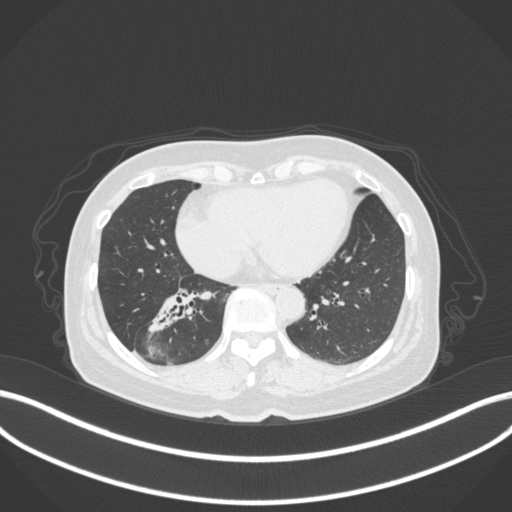
Chest CT, one axial slice; position 143 of 429 along the scan axis; reconstruction kernel B31f; lung window (W 1500 / L -600 HU); 512 × 512 image matrix. Female patient, age 67 years. From the clinical record (not read from this slice): clinical TNM (as recorded): T1c N1 M0; histopathological grade: G2-3.
Annotated regions visible in this slice (rectangle marked by the reading radiologist):
- lung tumour (recorded histology: adenocarcinoma): bounding box <141,282,200,335> (left, top, right, bottom; pixels)